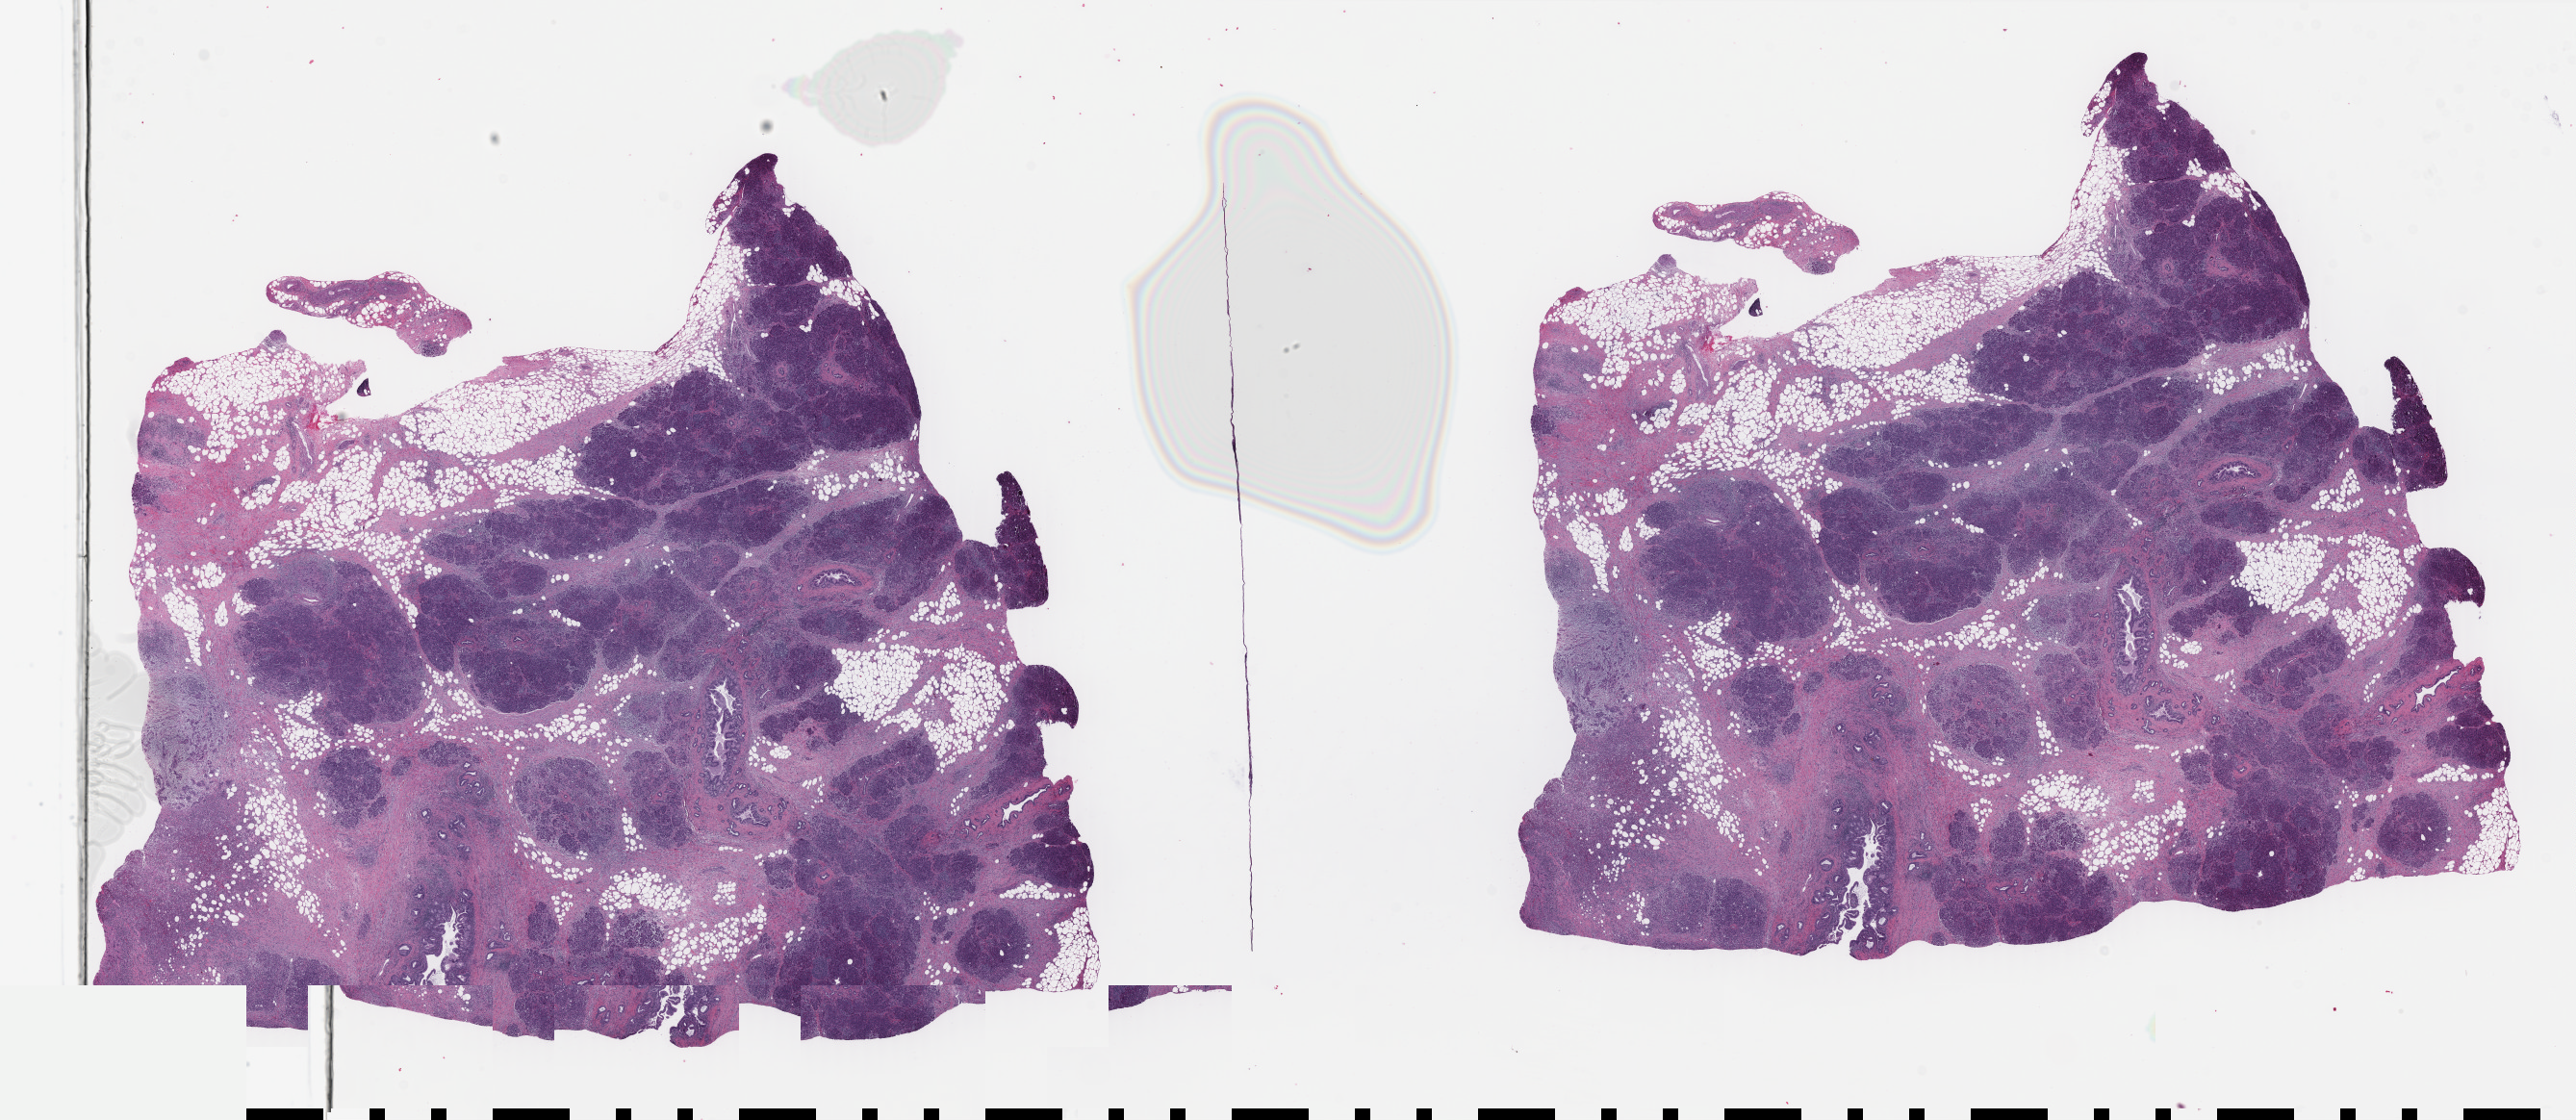
H&E-stained whole-slide image — shown as a low-resolution overview of the whole scanned area (about 42.4 x 18.4 mm, slide scanned at 40x). Formalin-fixed paraffin-embedded (FFPE) diagnostic section. Sample: primary tumour, pancreas. Male patient; age at initial diagnosis 77 years. Histologic grade: G3 (poorly differentiated).
* AJCC pathologic stage: IIB (7th edition)
* TNM: T3 N1 M0
* histologic diagnosis: Infiltrating duct carcinoma, NOS (head of pancreas)
* lymph nodes positive (case pathology): 7 of 19 examined